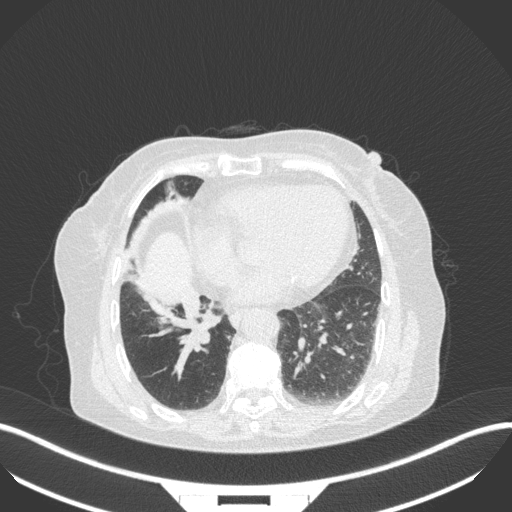
Chest CT, one axial slice; position 113 of 329 along the scan axis; reconstruction kernel B31f; 120 kVp; lung window (W 1500 / L -600 HU); 512 × 512 image matrix, field of view 400 × 400 mm. Patient: female, 75 years. From the clinical record (not read from this slice): clinical TNM (as recorded): T1b N0 M1a; histopathological grade: G1.
Annotated regions visible in this slice (bounding box drawn by a radiologist):
- lung tumour (recorded histology: squamous cell carcinoma): bounding box <185,306,219,353> (left, top, right, bottom; pixels)